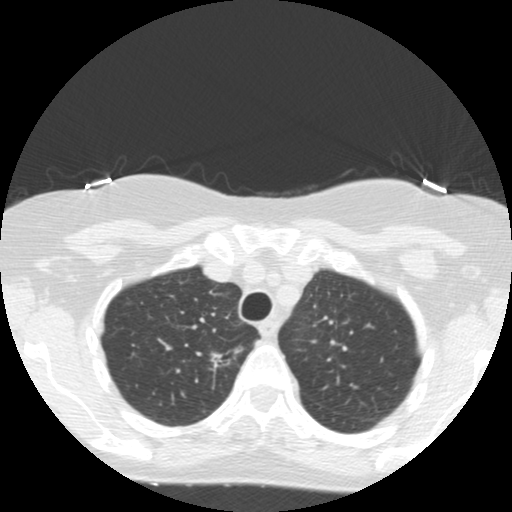
Low-dose screening chest CT, one axial slice. Position 122 of 155 along the scan axis. Lung window (W 1500 / L -600 HU). 2.5 mm slice thickness. 512 × 512 image matrix.
Structures marked on this image (outlined manually by an expert reader):
- lesion 1 (tumor, upper lobe of right lung): bounding box [x1, y1, x2, y2] px = [211, 353, 231, 372]